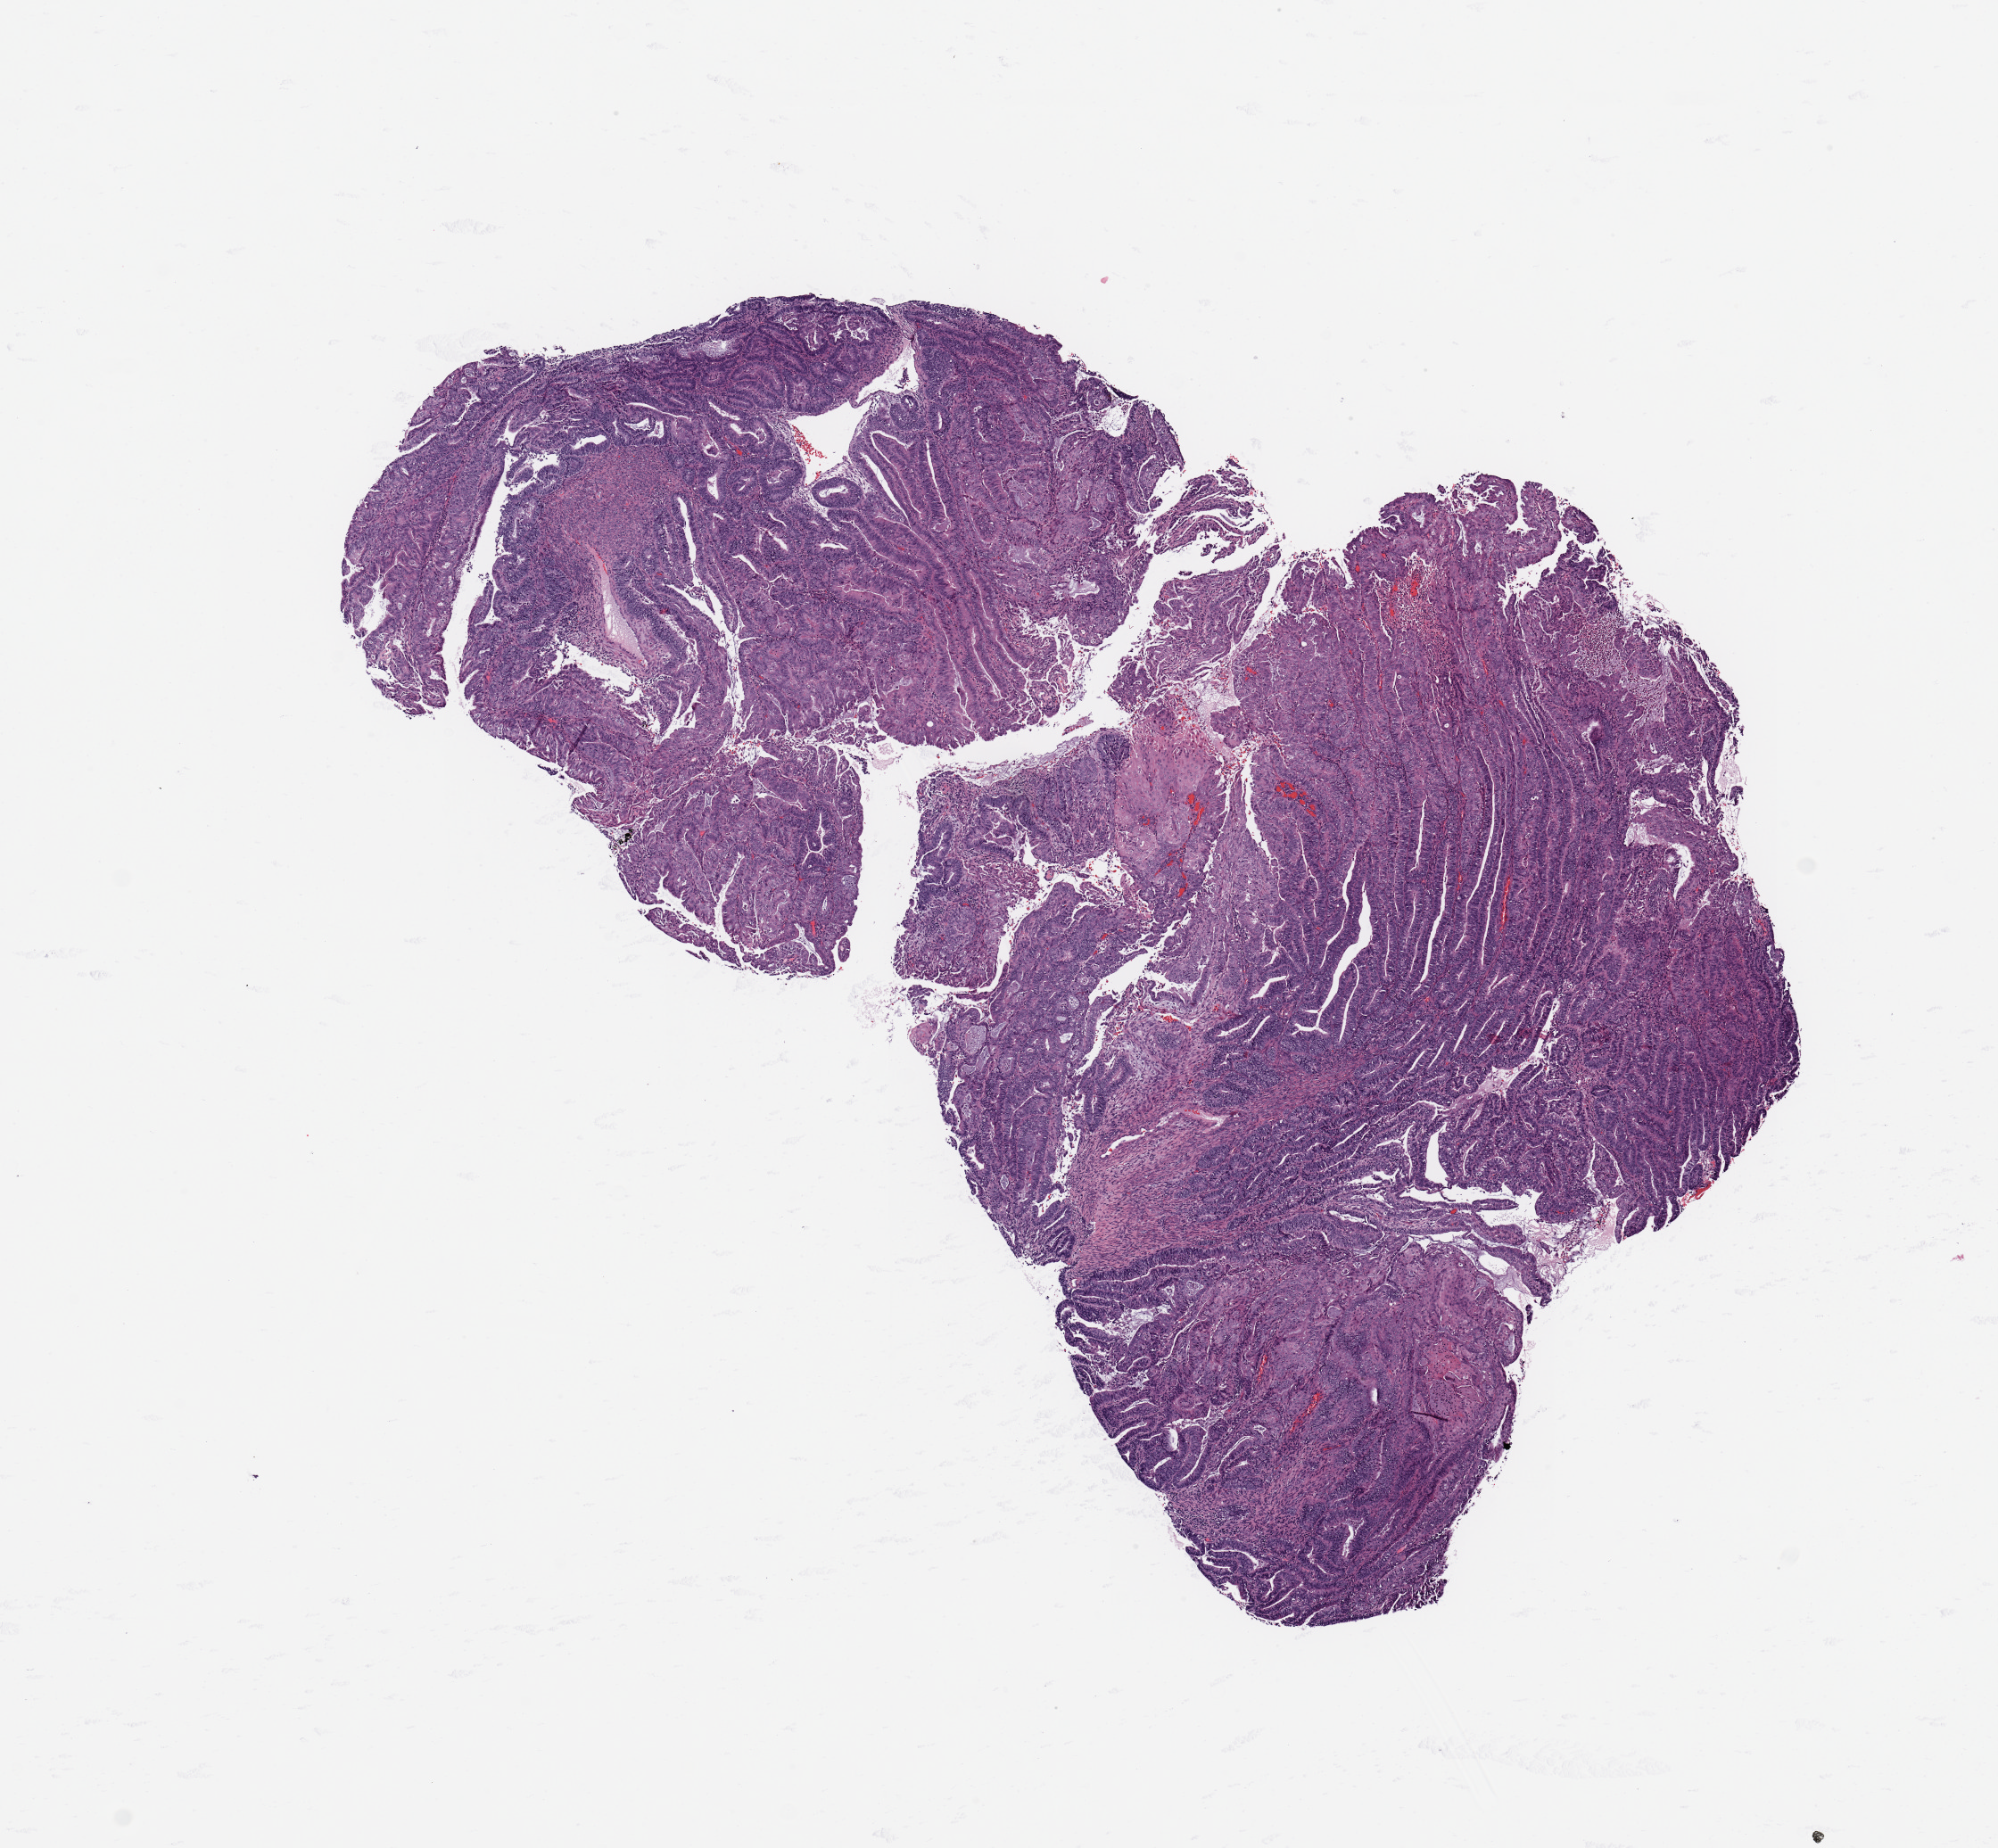
Whole-slide histology image, H&E, a low-resolution overview of the entire scanned area, about 8.9 x 8.2 mm. Tumour tissue sample, sampled site: uterus. 64-year-old female patient. Histologic grade: G2 (moderately differentiated). Composition of this section per pathologist review: tumour nuclei 90%, necrosis 2%.
AJCC pathologic stage: III. Diagnosis: Endometrioid adenocarcinoma, NOS. Primary tumour site (as recorded): anterior endometrium.